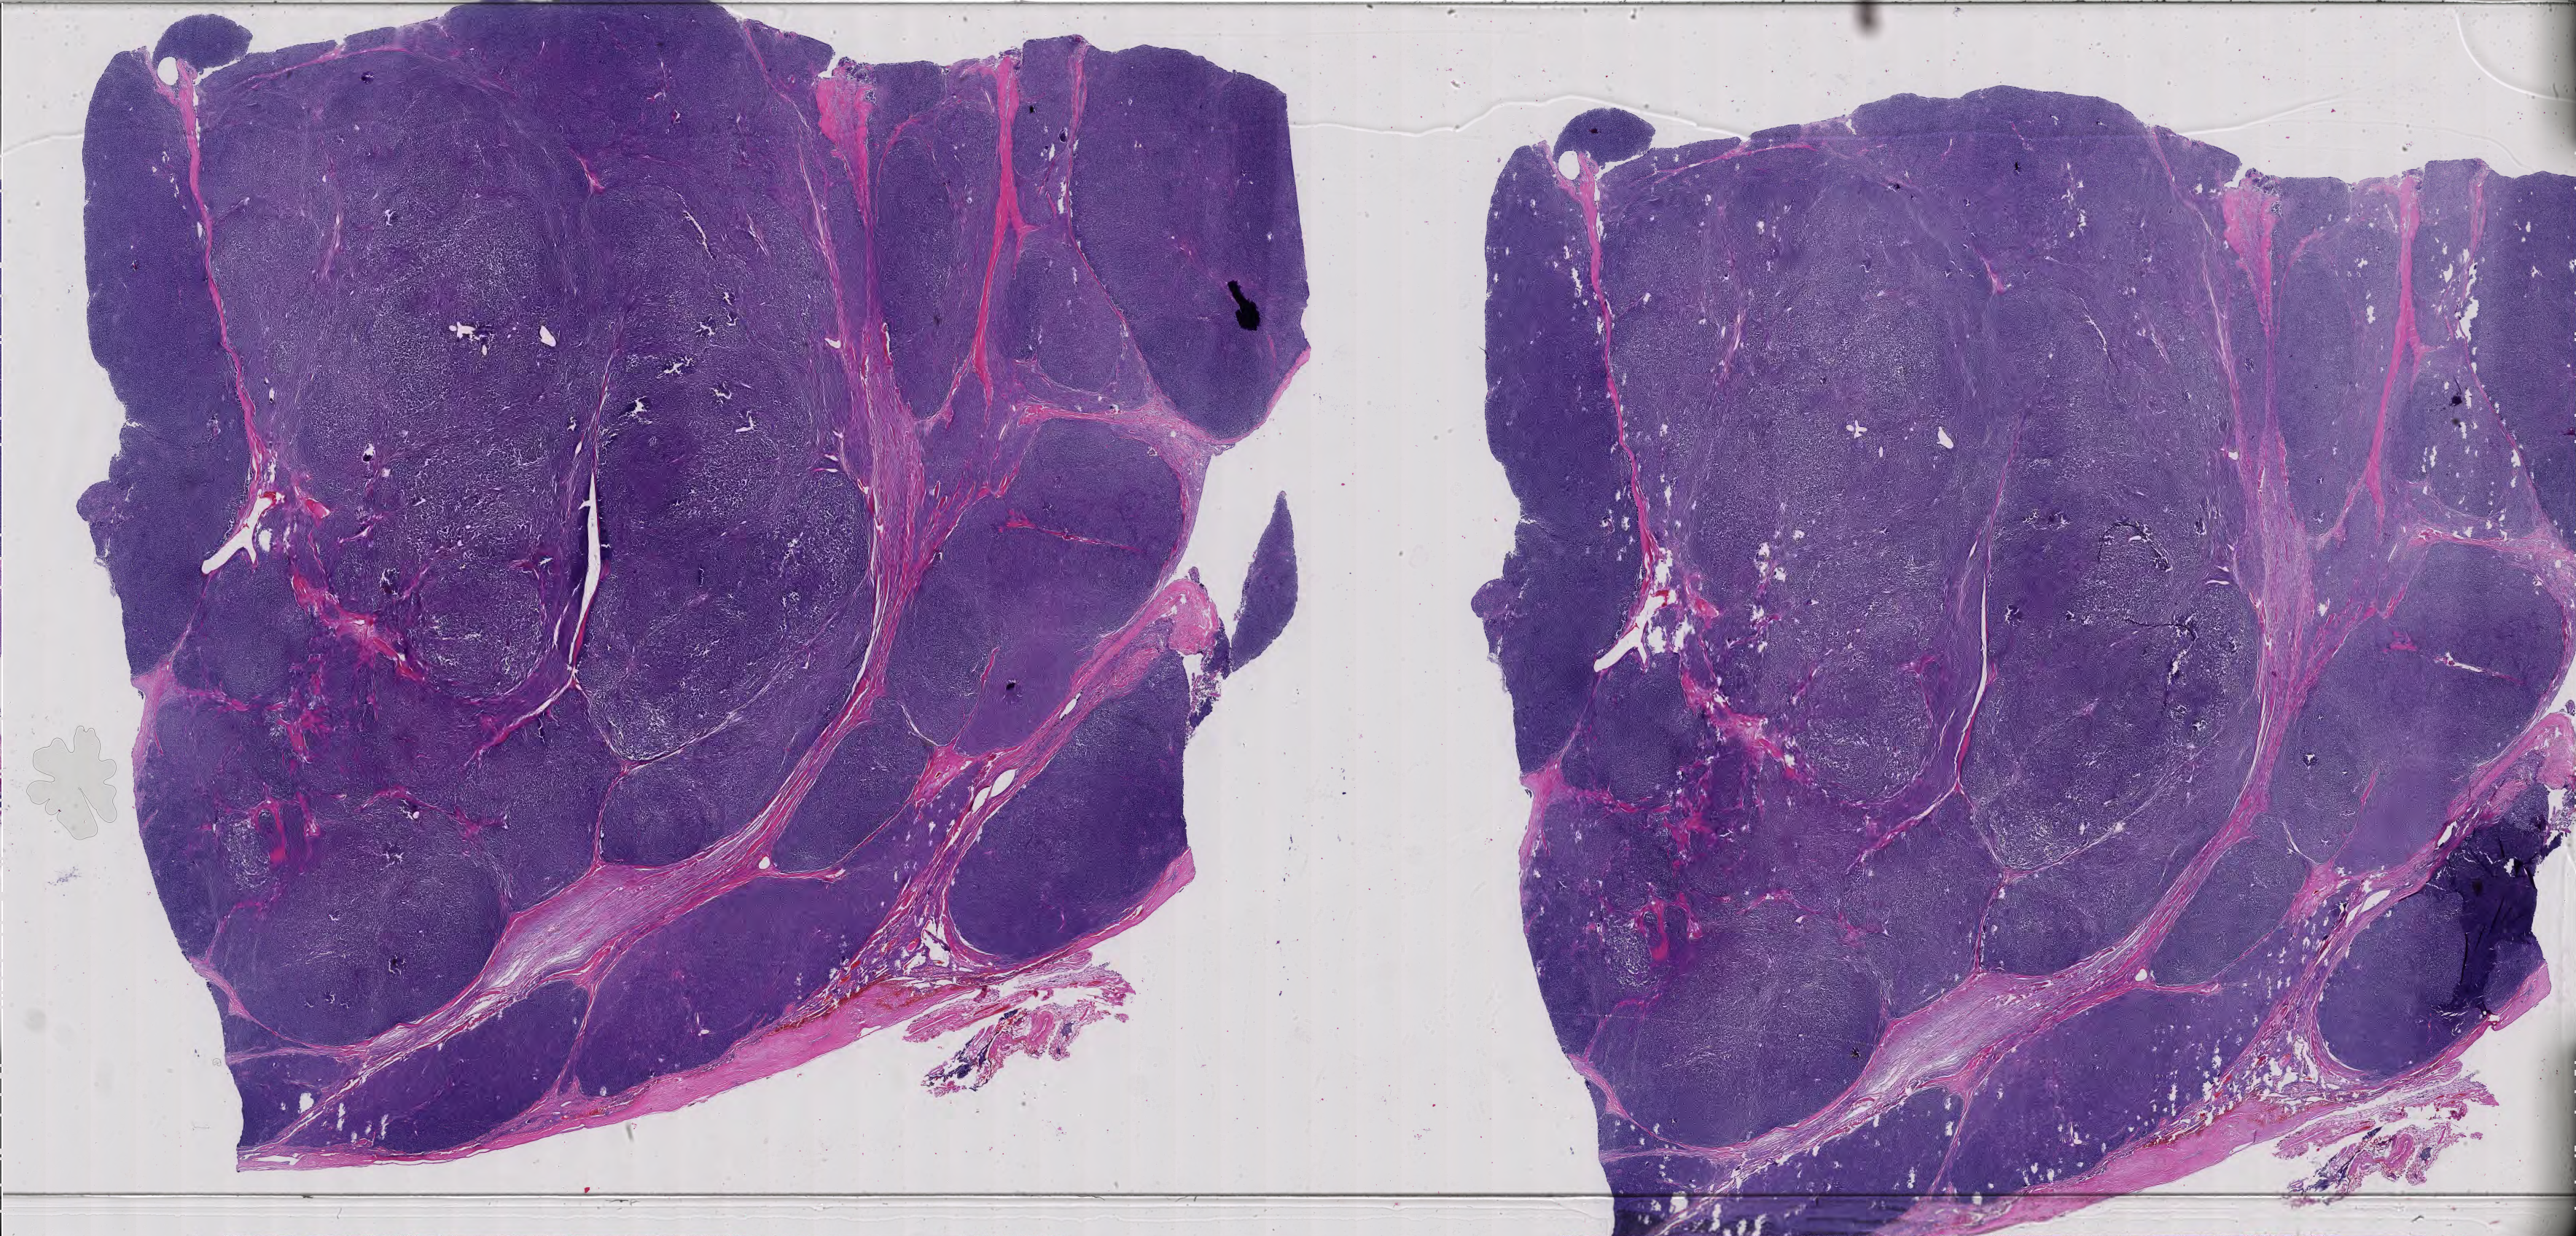
Whole-slide histology image, H&E-stained, whole scanned area (about 51.5 x 24.7 mm, from a 40x scan) shown as a low-resolution overview; formalin-fixed paraffin-embedded (FFPE) diagnostic section; sample: primary tumour, thymus. Male patient; age at initial diagnosis 69 years.
* diagnosis: Thymoma, type AB, malignant